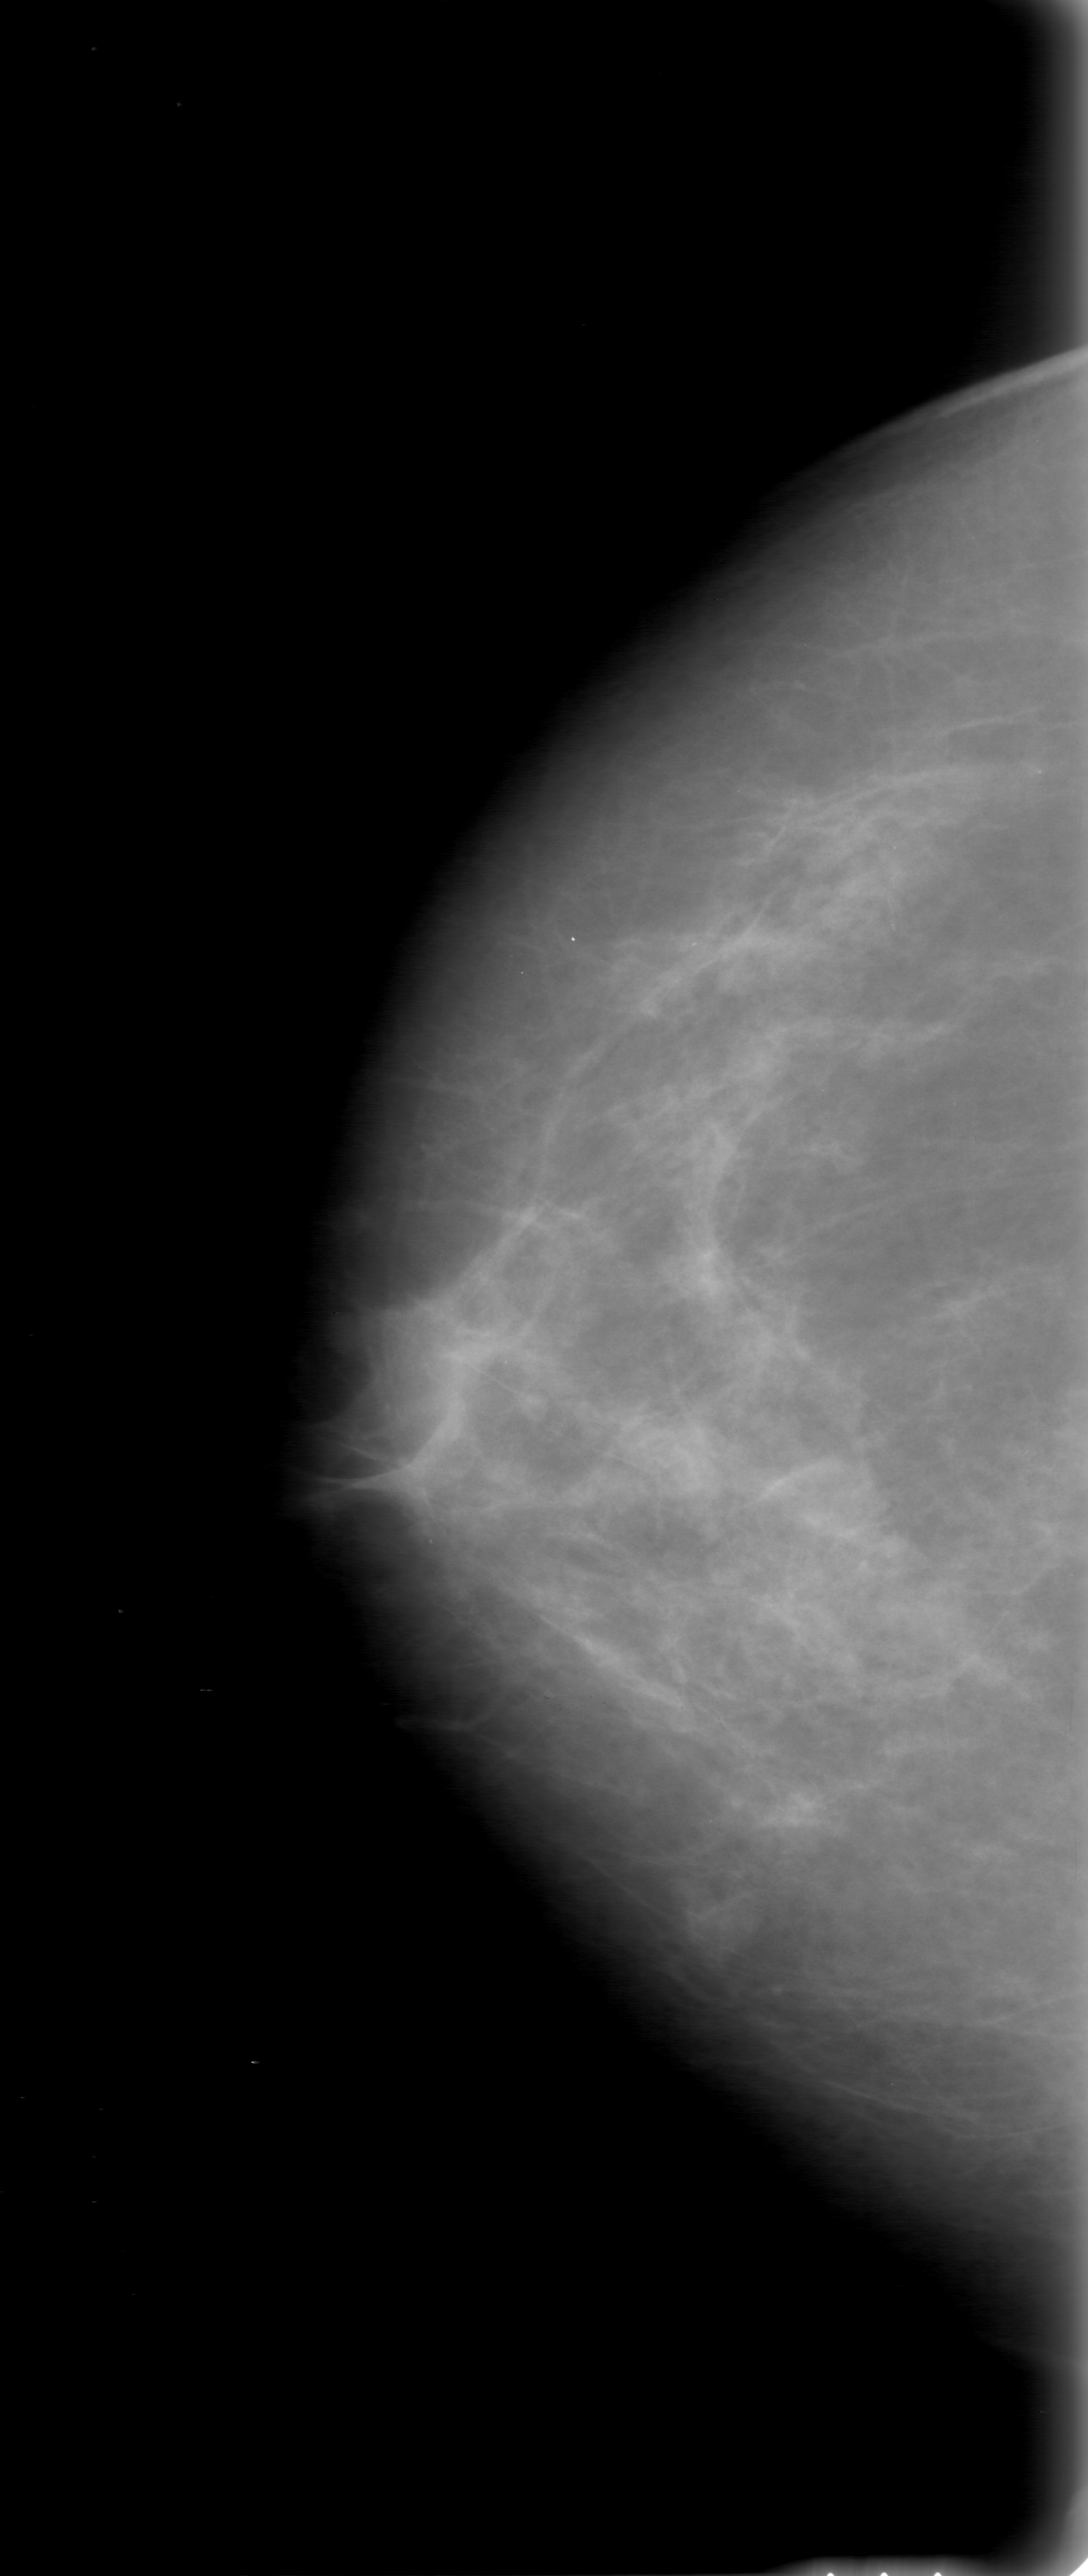
Digitized screen-film mammogram; right breast; craniocaudal (CC) view; BI-RADS breast density category 2 (scale 1–4); 1088 × 2576 image matrix.
Expert-marked regions of interest on this film, with their recorded descriptors:
- mass, shape oval, margins obscured; BI-RADS assessment category 0 (incomplete: needs additional imaging); subtlety rating 4 on a 1 (subtle) to 5 (obvious) scale; pathology result (as recorded, not read from the image): benign: bounding box [x1, y1, x2, y2] px = [675, 1863, 774, 1963]